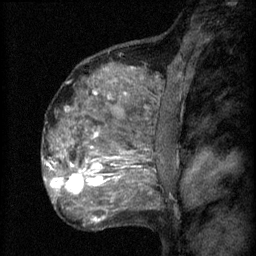
Breast MRI (dynamic contrast-enhanced), one sagittal slice. Position 42 of 60 along the scan axis. 3 images stored at this slice position (order not interpretable as contrast timing). 1.5 T. TE 4.2 ms, TR 8.2 ms. 2 mm slice thickness. 256 × 256 image matrix. Patient: female, 48 years.
Annotated regions visible in this slice (semi-automatically segmented with operator editing):
- analysis volume of interest (the breast-tissue region the enhancement analysis was run in; not a lesion): bounding box (x1, y1, x2, y2) in pixels: (61, 138, 152, 201)
- tumour enhancement mask (voxels above the 70 % enhancement threshold inside the analysis volume of interest): (61, 164, 119, 195)